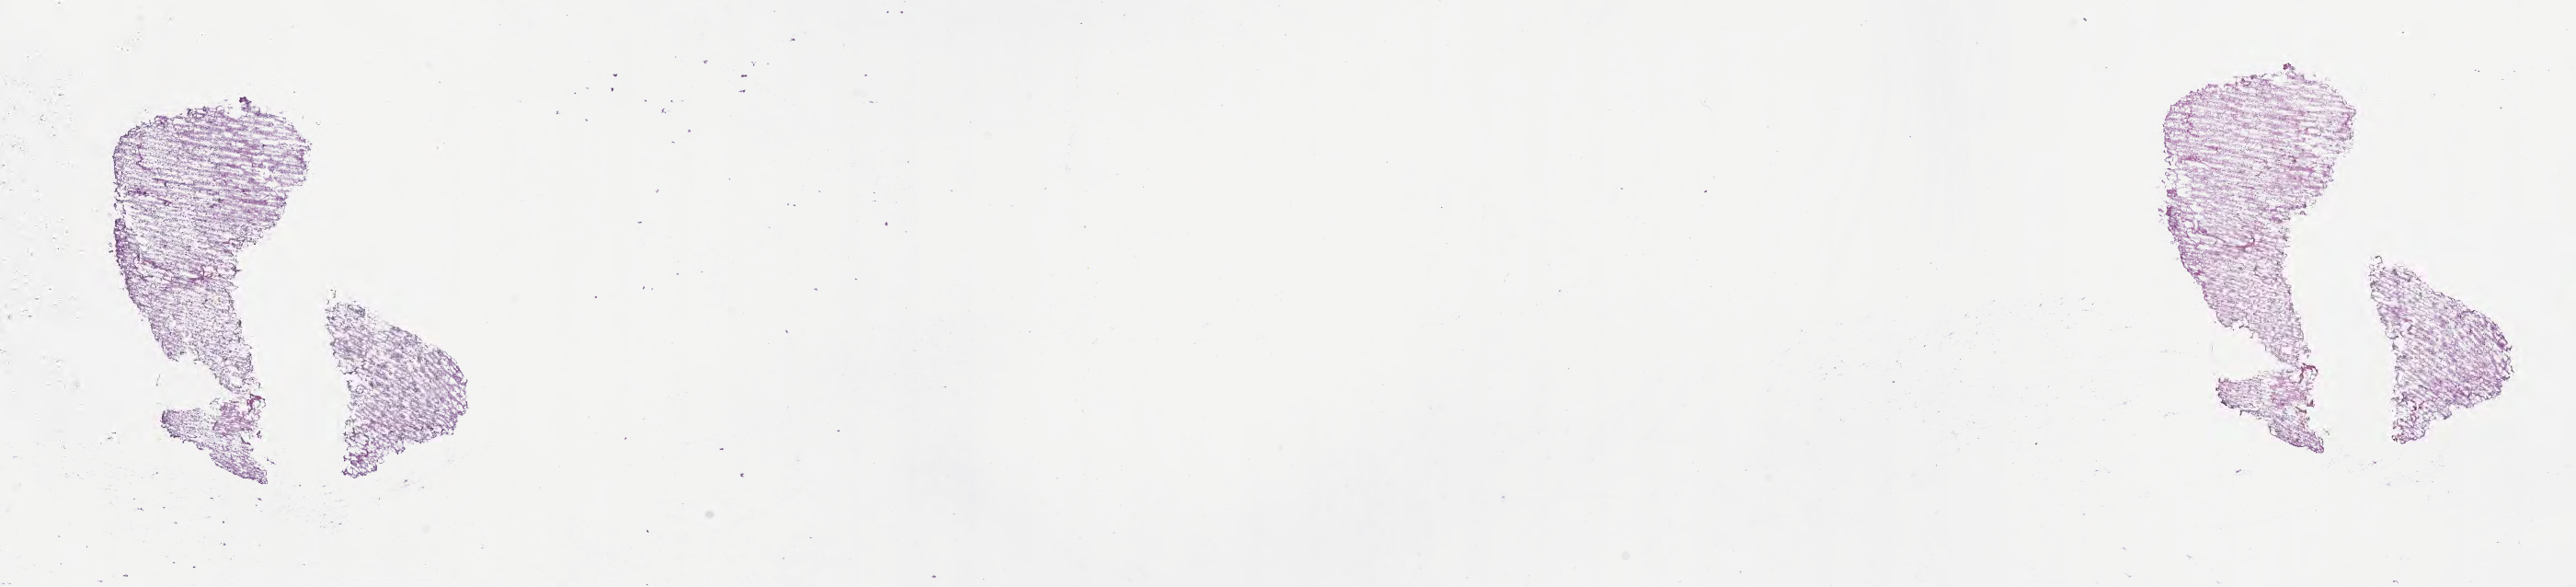
Digitized H&E-stained section of tumor tissue from the brain — low-resolution overview of the scanned area, about 22.6 x 5.2 mm, cryosection (OCT / tissue freezing medium). Female patient, age 42 months (3 years 6 months).
Diagnosis (ICD-O-3 morphology term): Pilocytic astrocytoma.